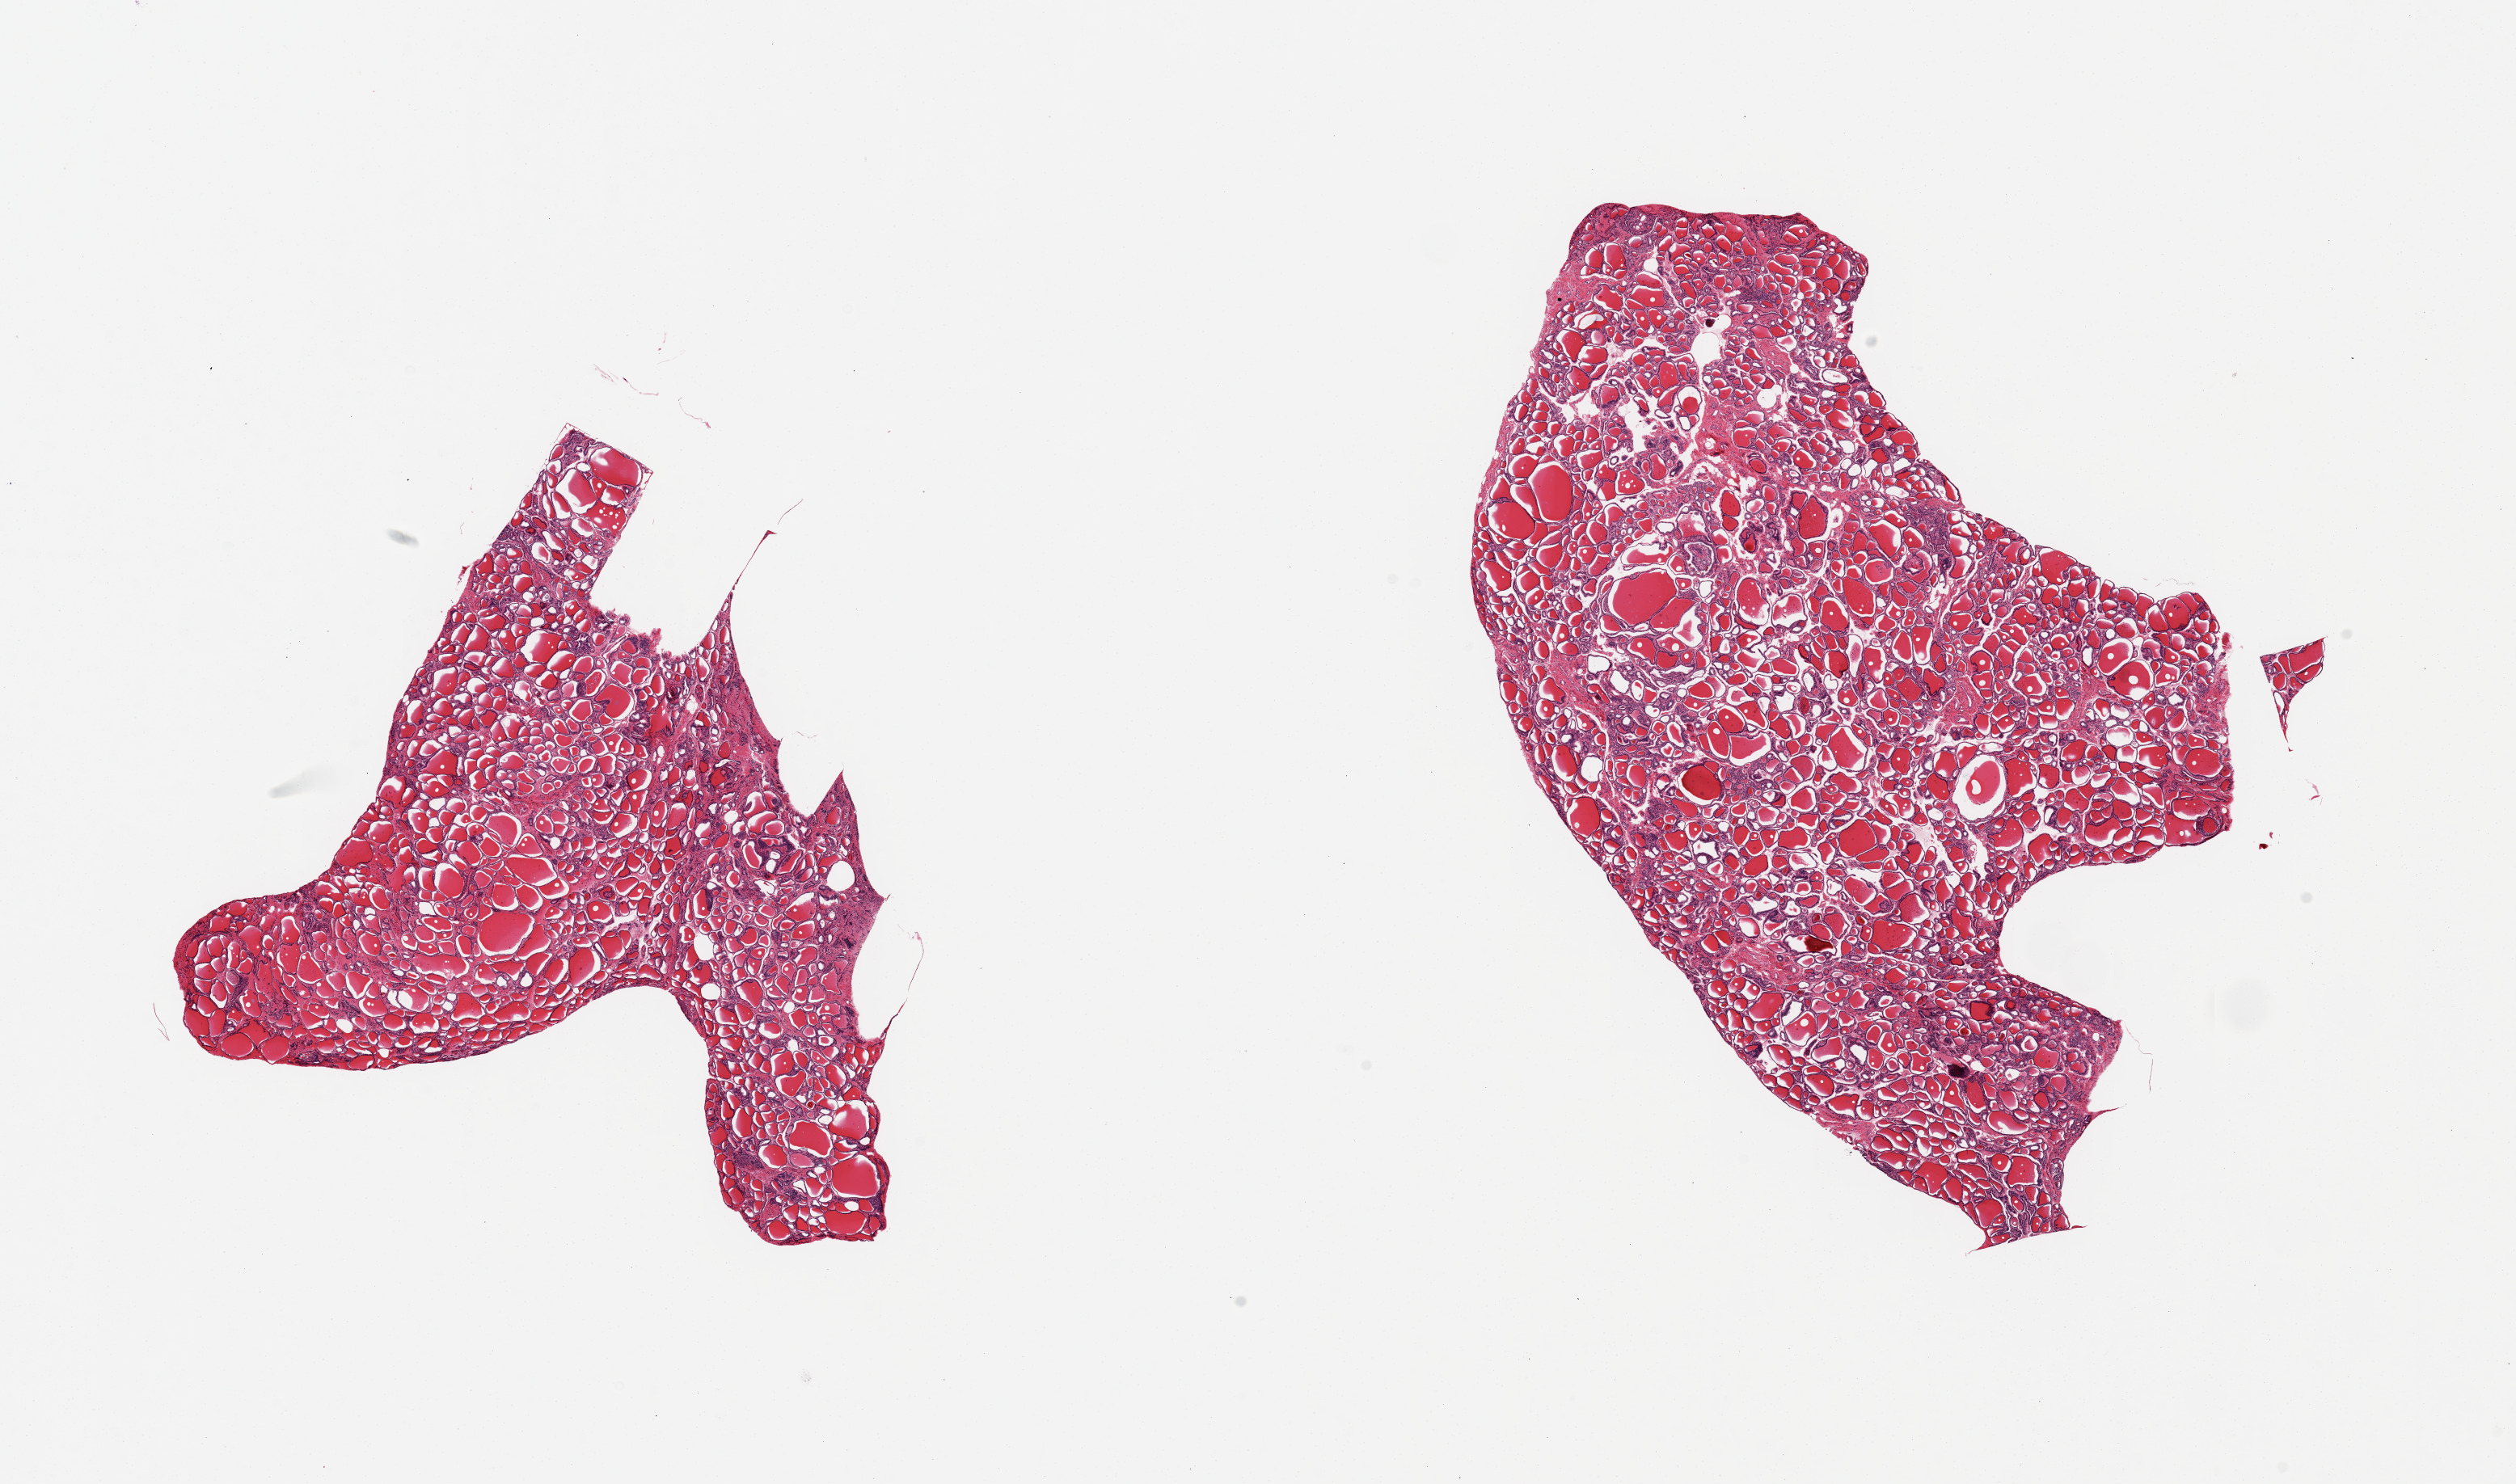
H&E whole-slide image — whole scanned area (about 24.6 x 14.5 mm, slide scanned at 20x) shown as a low-resolution overview; PAXgene-fixed paraffin-embedded (PFPE) section; target tissue: thyroid; tissue donor sample. Donor sex: female.
Pathologist's review note for this sample: 2 pieces, mild chronic inflammation, possible autoimmune thyroiditis.